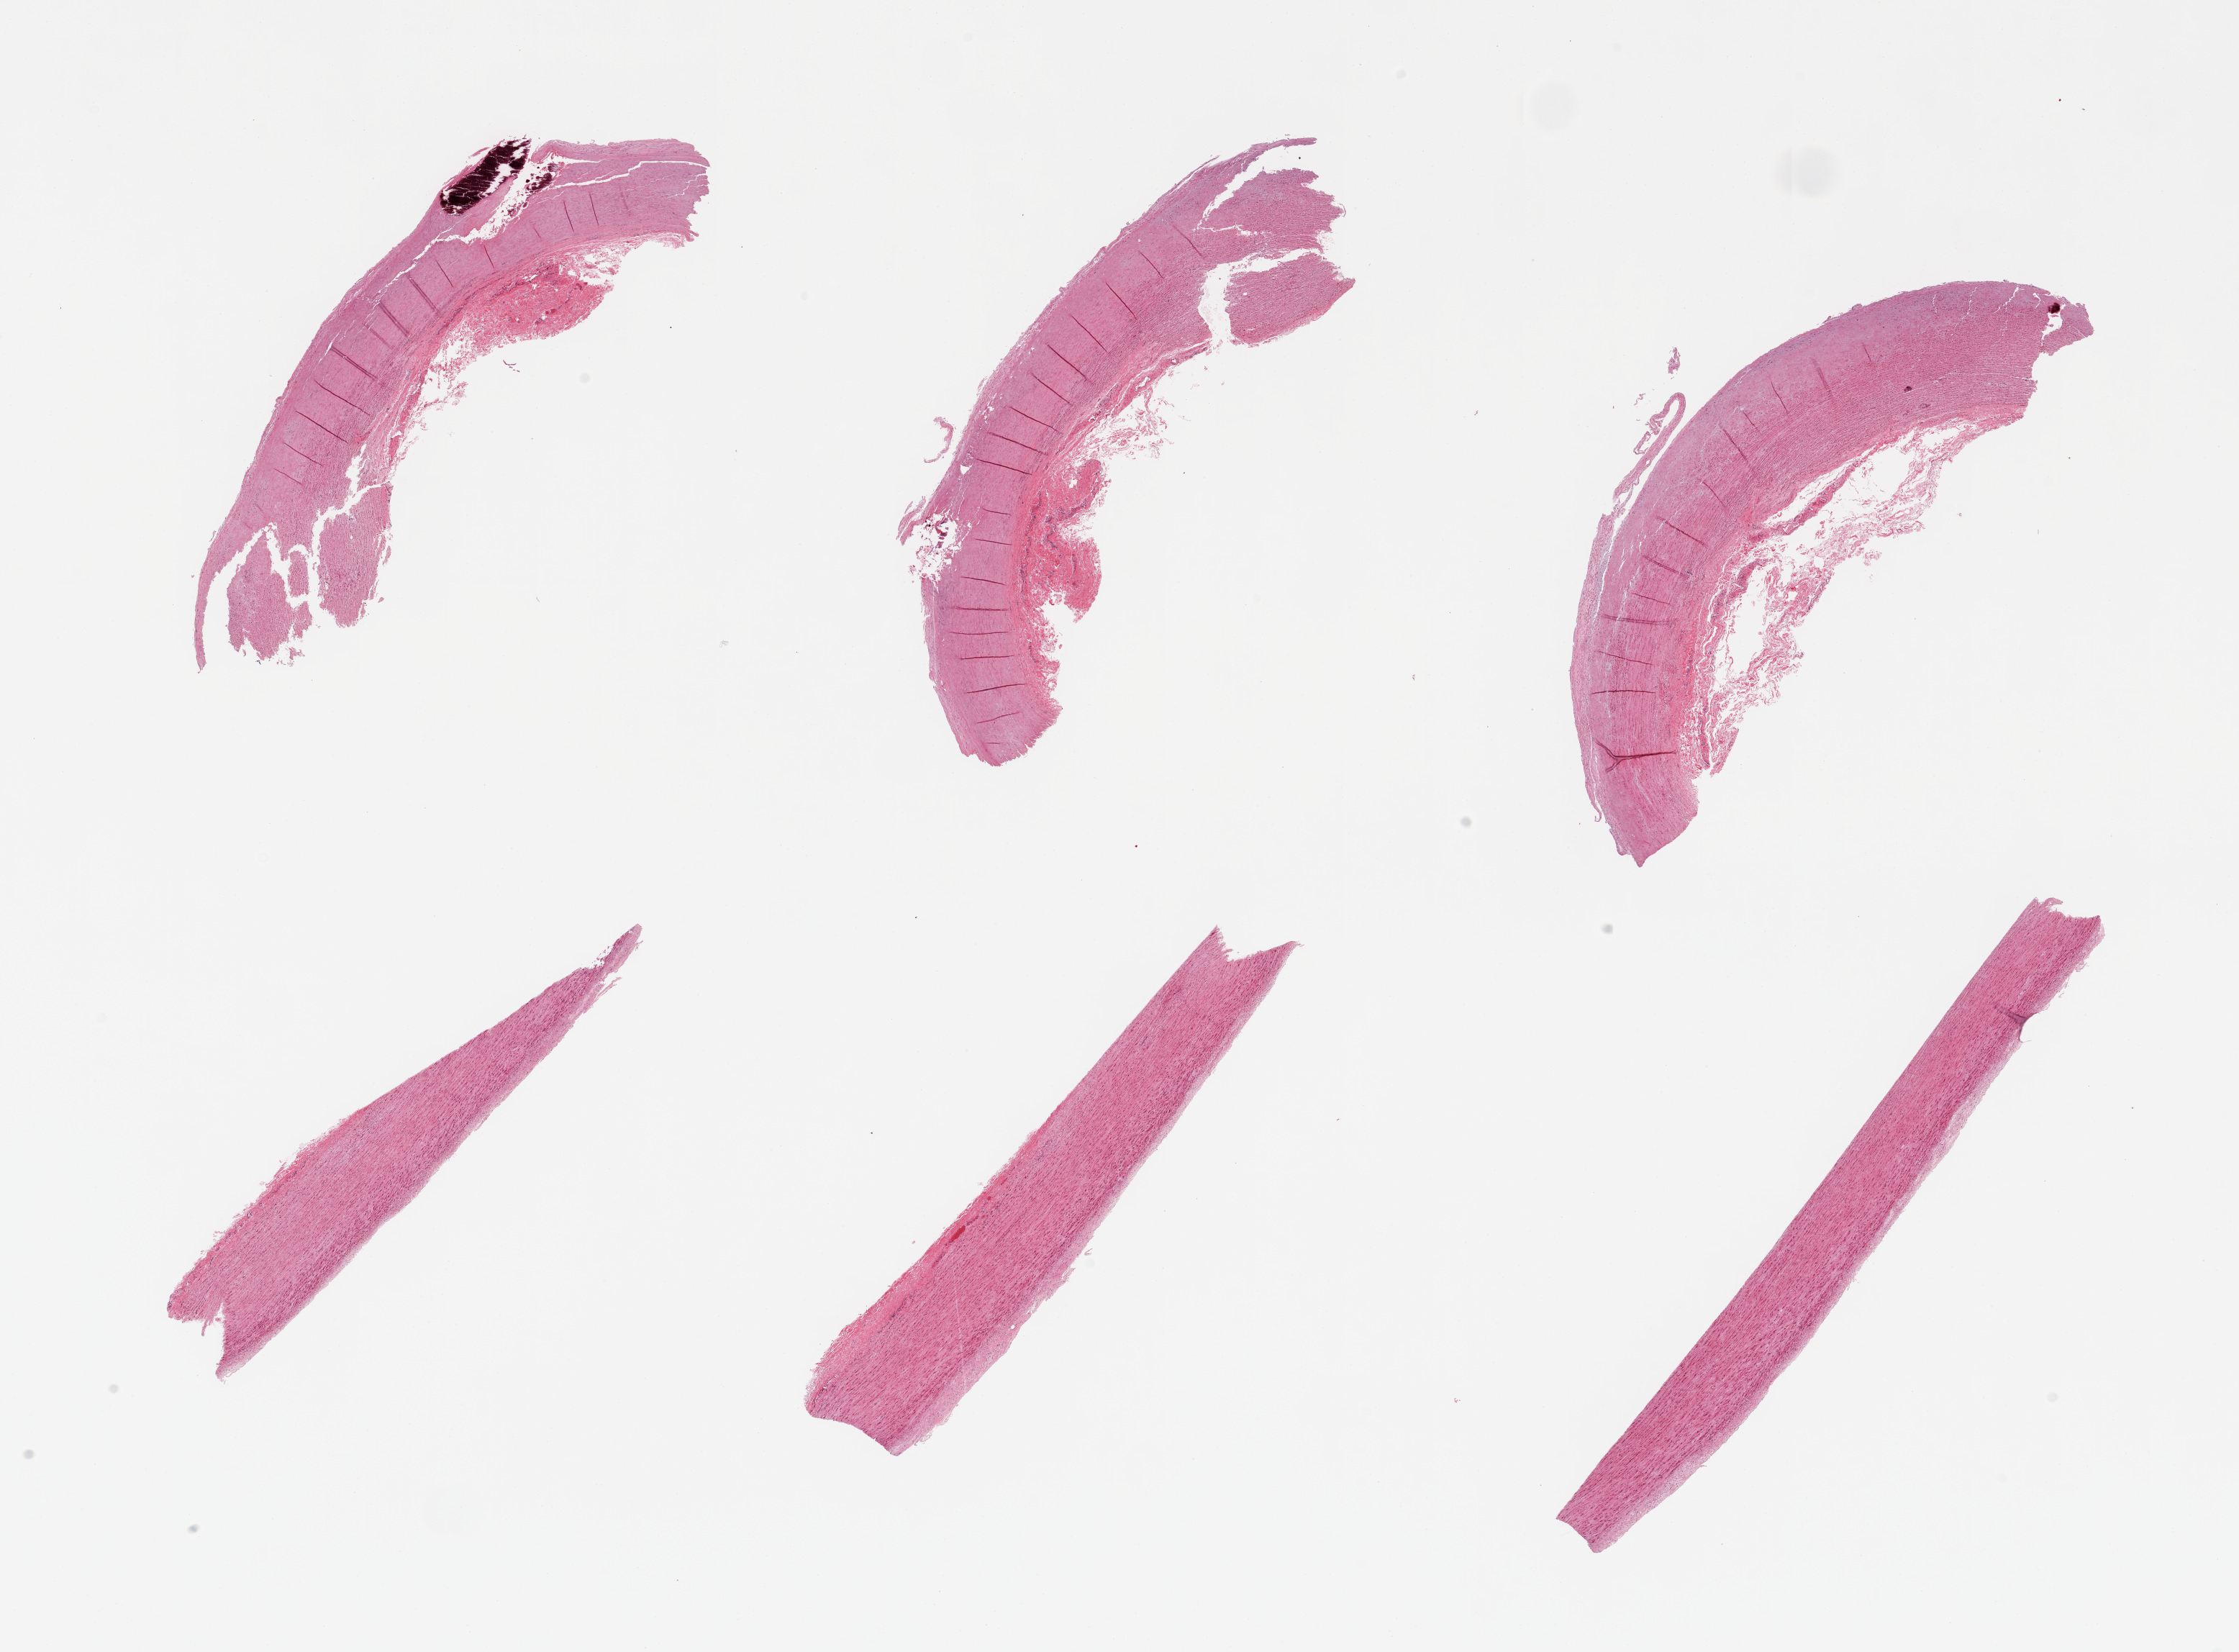
Whole-slide image, haematoxylin and eosin stain, brightfield — a low-resolution overview of the entire scanned area, about 24.6 x 18.2 mm (from a 20x scan), PAXgene-fixed paraffin-embedded (PFPE) section, section of aorta (target tissue), donor tissue sample.
Pathologist's review note for this sample: 6 pieces; calcific atherosclerosis.